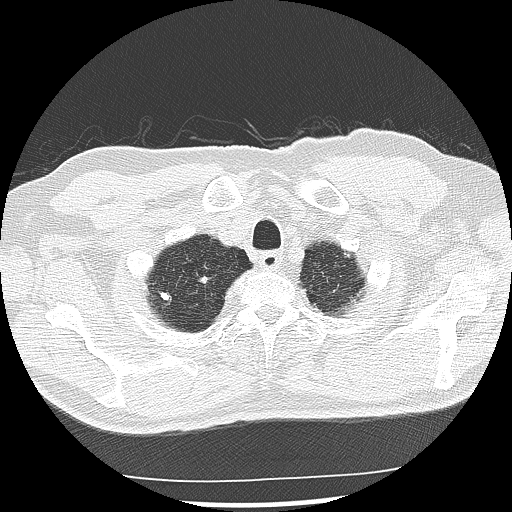
Low-dose screening chest CT, one axial slice; slice 125 of 142 in the series (ordered by position); lung window (W 1500 / L -600 HU); 512 × 512 image matrix, field of view 360 × 360 mm.
Annotated regions visible in this slice (expert manual segmentation):
- lesion 3 (nodule, upper lobe of right lung): box from (x=197, y=274) to (x=211, y=284) px